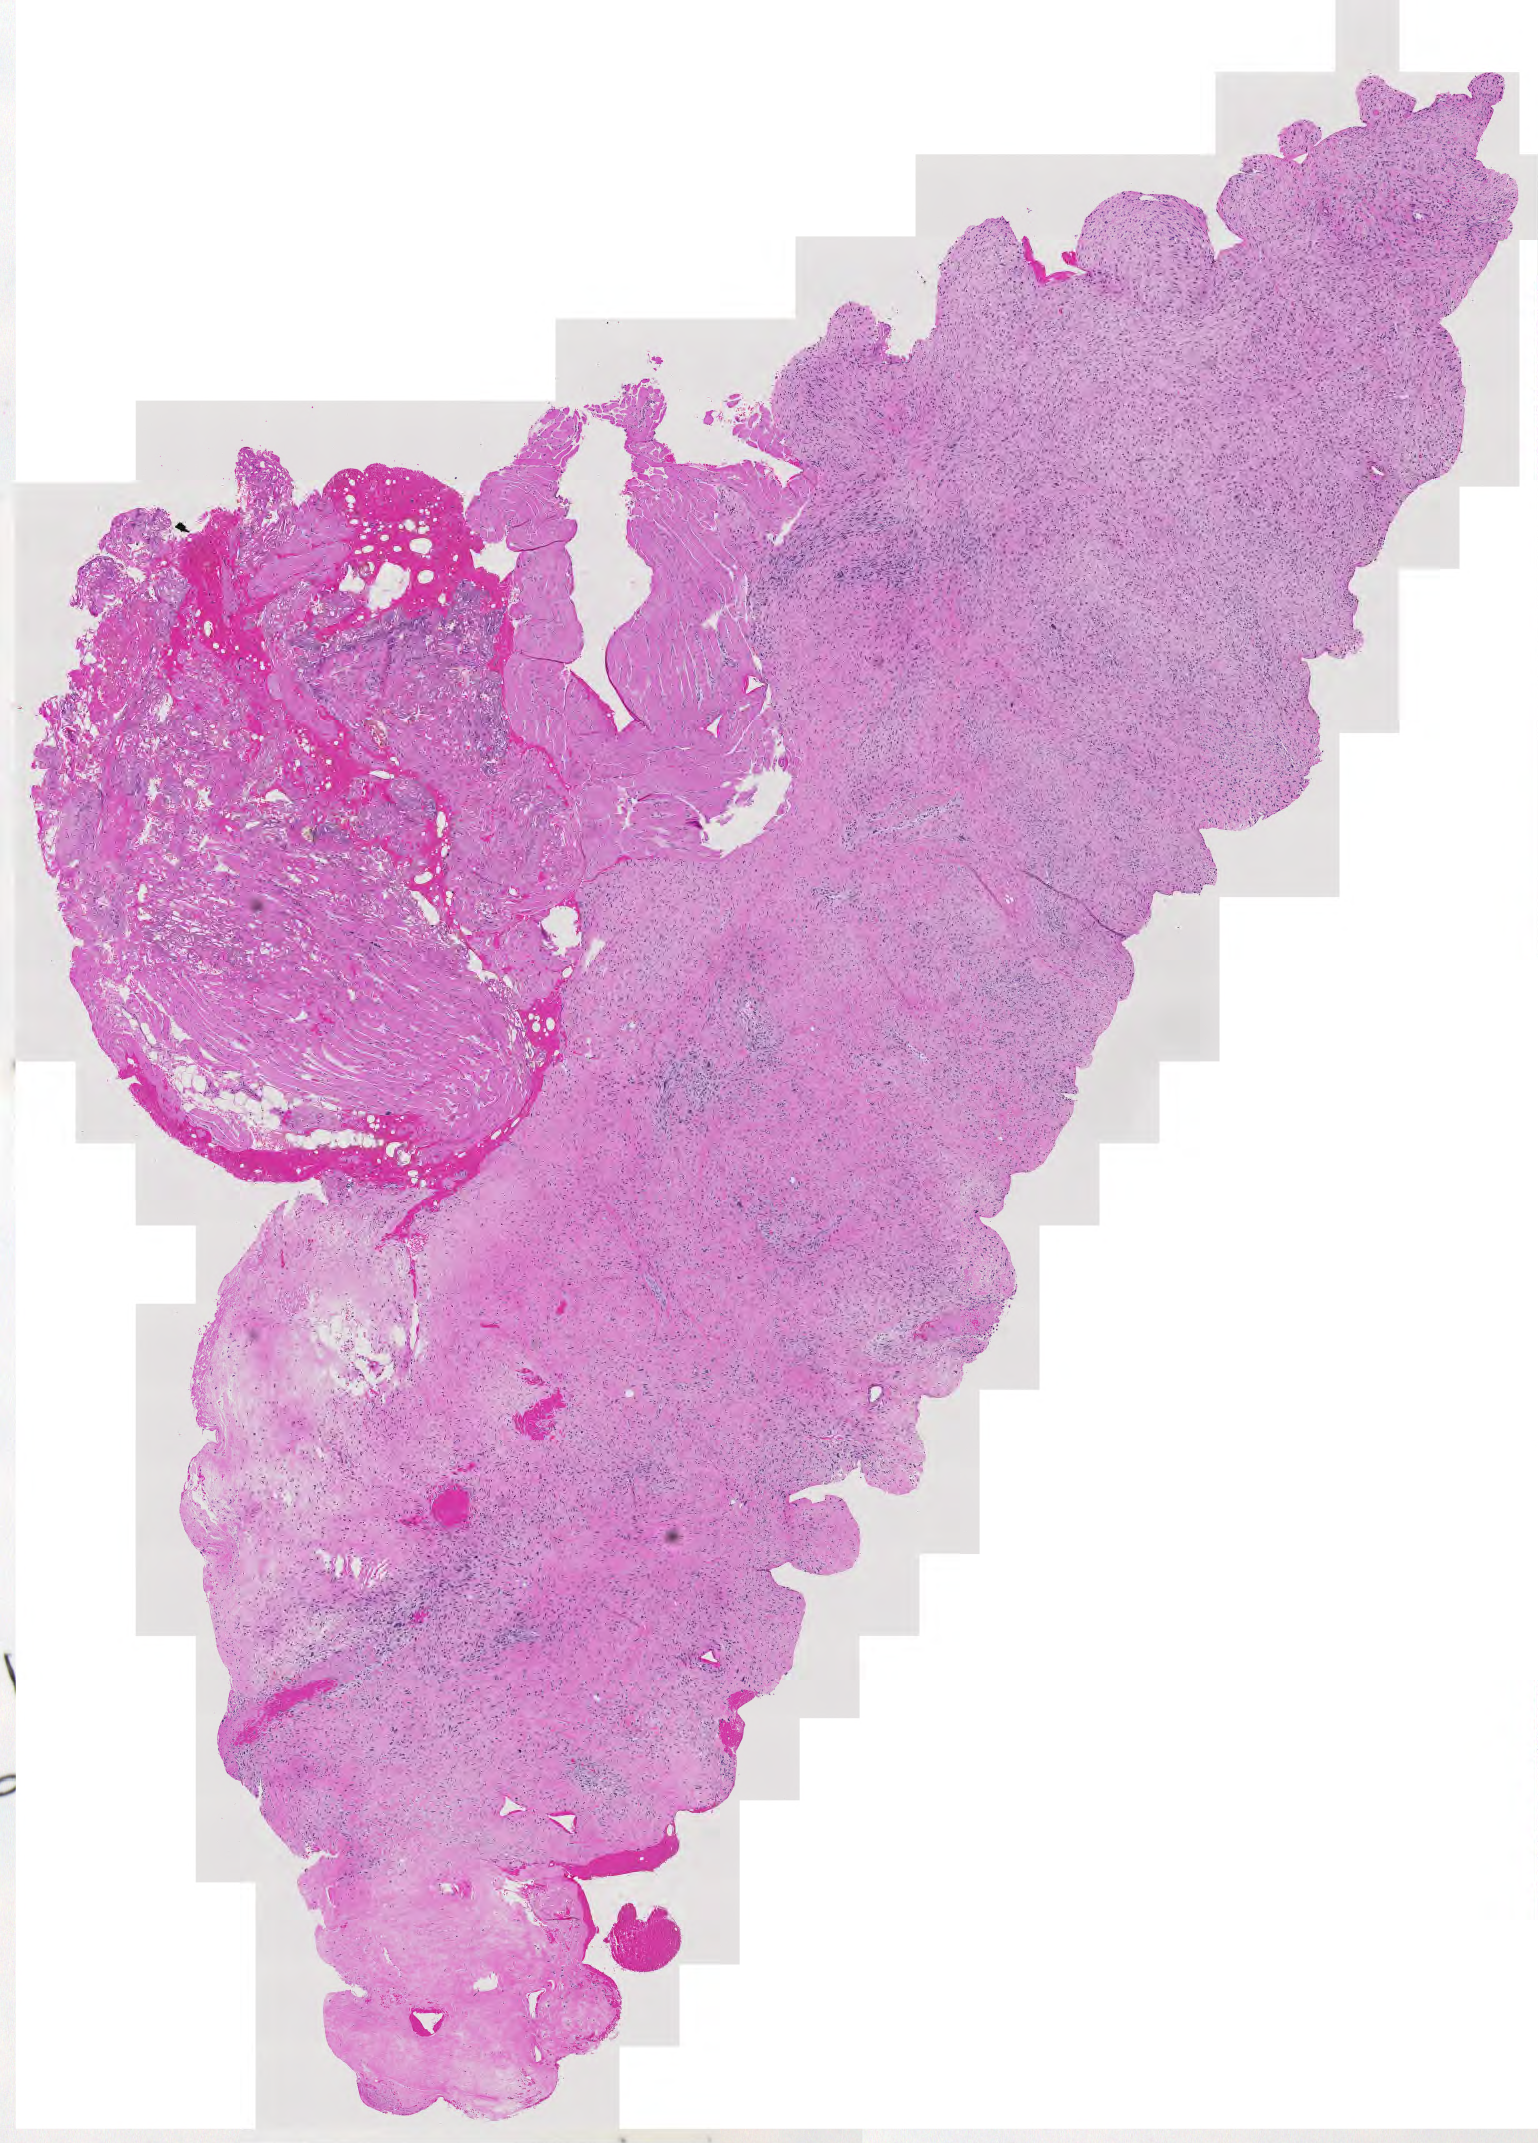
Whole-slide histology image, Hematoxylin and eosin (H&E) stained — a low-resolution overview of the entire scanned area, about 7.9 x 11.1 mm, tumour tissue sample. Patient: female, age 75 years.
• primary tumour site (as recorded): lower extremity
• patient diagnosis (cohort enrolment): sarcoma (site not recorded at cohort level)